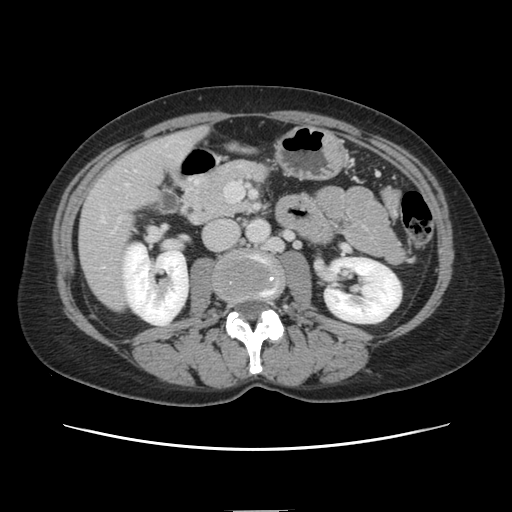
Contrast-enhanced abdominal CT, one axial slice; position 46 of 141 along the scan axis; 120 kVp; intravenous contrast given; soft-tissue window (W 400 / L 40 HU); 512 × 512 image matrix. Female patient, age 63 years. From the clinical record (not read from this slice): diagnosis: colorectal cancer liver metastases, imaged before liver resection; multiple liver metastases: yes.
Annotated regions visible in this slice (manually delineated by an expert):
- liver: box from (x=80, y=130) to (x=203, y=310) px
- planned liver remnant (the part of the liver to remain after resection): (x=181, y=130)–(x=204, y=156)
- portal vein (with intrahepatic branches): (x=102, y=219)–(x=104, y=221)